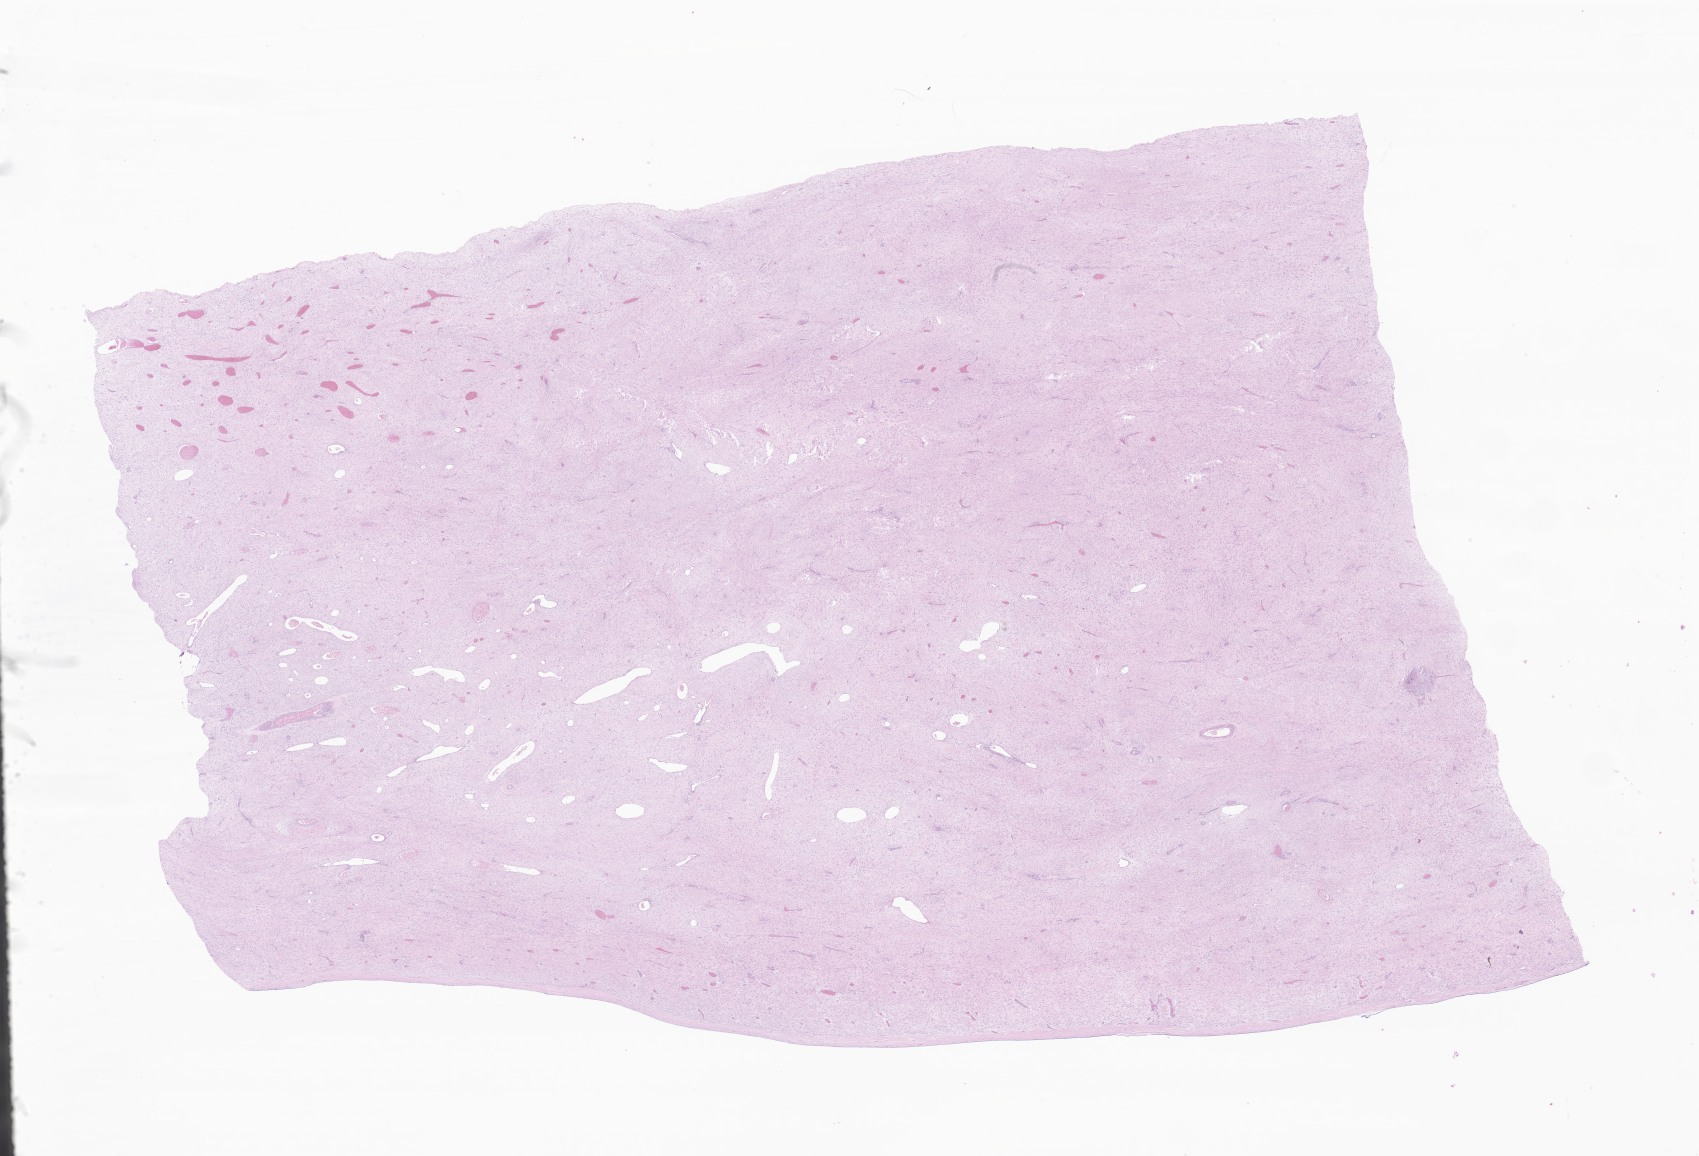
Whole-slide image, H&E stain of tumor tissue from the abdomen — low-resolution overview of the scanned area, about 28.7 x 19.5 mm; FFPE section. Patient female; age 214 months (17 years 10 months).
Diagnosis: Aggressive fibromatosis.